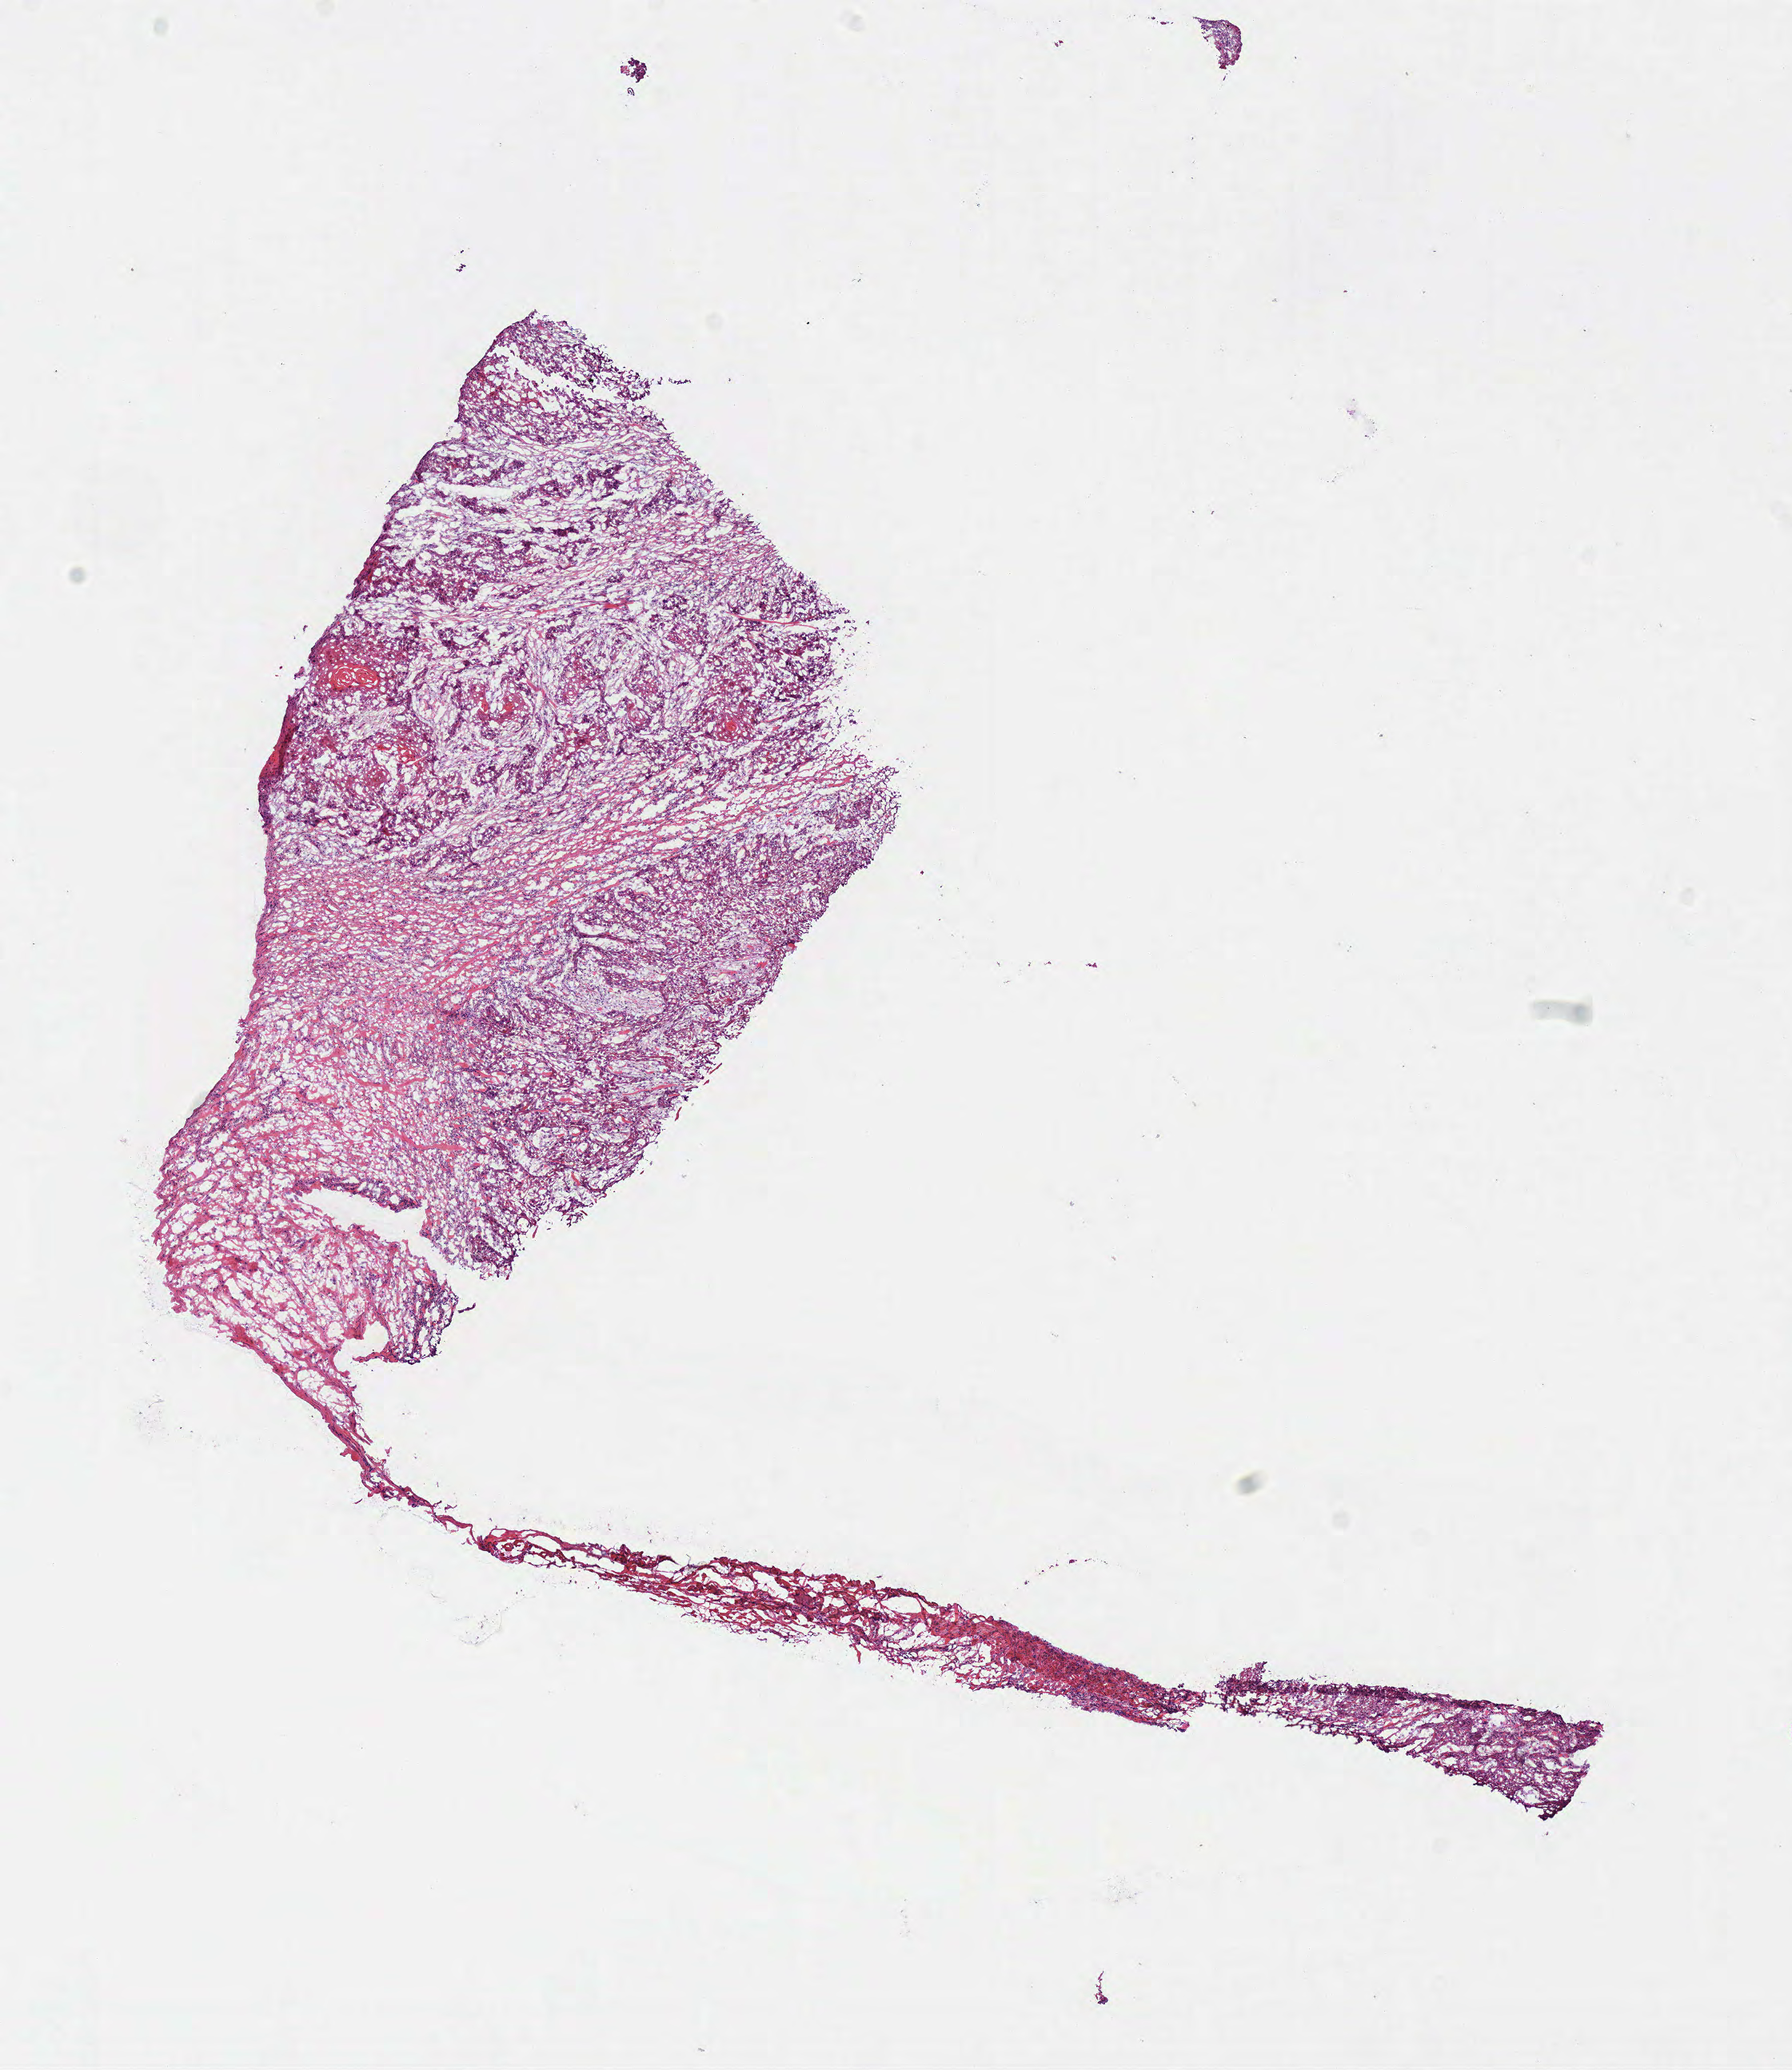
Whole-slide histology image, H&E-stained — shown as a low-resolution overview of the whole scanned area (about 8.8 x 10.2 mm, slide scanned at 40x). Frozen section. Sample: primary tumour, head and neck. Female, age 87 years at initial diagnosis. Histologic grade: G2 (moderately differentiated). Composition of this section per pathologist review: tumour cells 62%, tumour nuclei 60%, normal cells 8%, stromal cells 30%, necrosis 0%.
• TNM: T2 NX
• AJCC pathologic stage: II (7th edition)
• diagnosis: Squamous cell carcinoma, NOS (overlapping lesion of lip, oral cavity and pharynx)